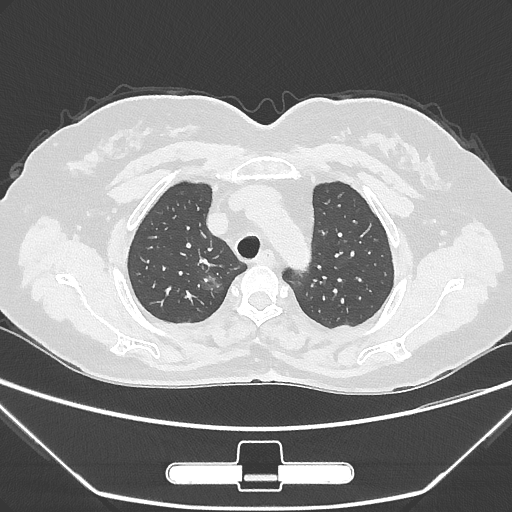
Chest CT, one axial slice. Slice 226 of 275 in the series (ordered by position). Lung window (W 1500 / L -600 HU). 512 × 512 image matrix, field of view 356 × 356 mm. Patient: female, 63 years. From the clinical record (not read from this slice): clinical TNM (as recorded): T1a N0 M0; histopathological grade: G1.
Annotated regions visible in this slice (rectangle marked by the reading radiologist):
- lung tumour (recorded histology: adenocarcinoma): bounding box <197,265,233,301> (left, top, right, bottom; pixels)